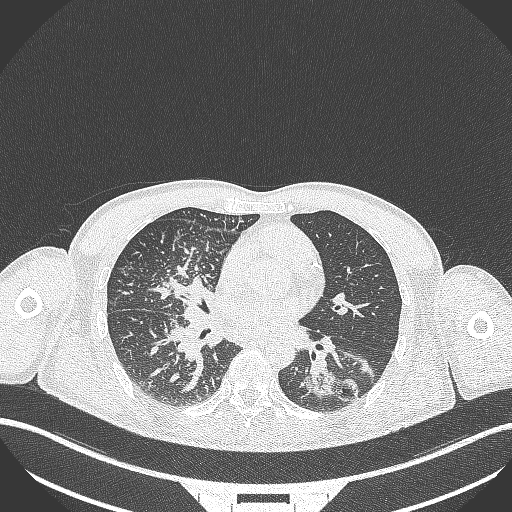
Chest CT, one axial slice. Slice 153 of 348 in the series (ordered by position). 120 kVp. Lung window (W 1500 / L -600 HU). 1 mm slice thickness. 512 × 512 image matrix, field of view 400 × 400 mm. Patient: male, 49 years. From the clinical record (not read from this slice): clinical TNM (as recorded): T2b N1 M0.
Structures marked on this image (bounding box drawn by a radiologist):
- lung tumour (recorded histology: adenocarcinoma): box from (x=303, y=361) to (x=363, y=409) px